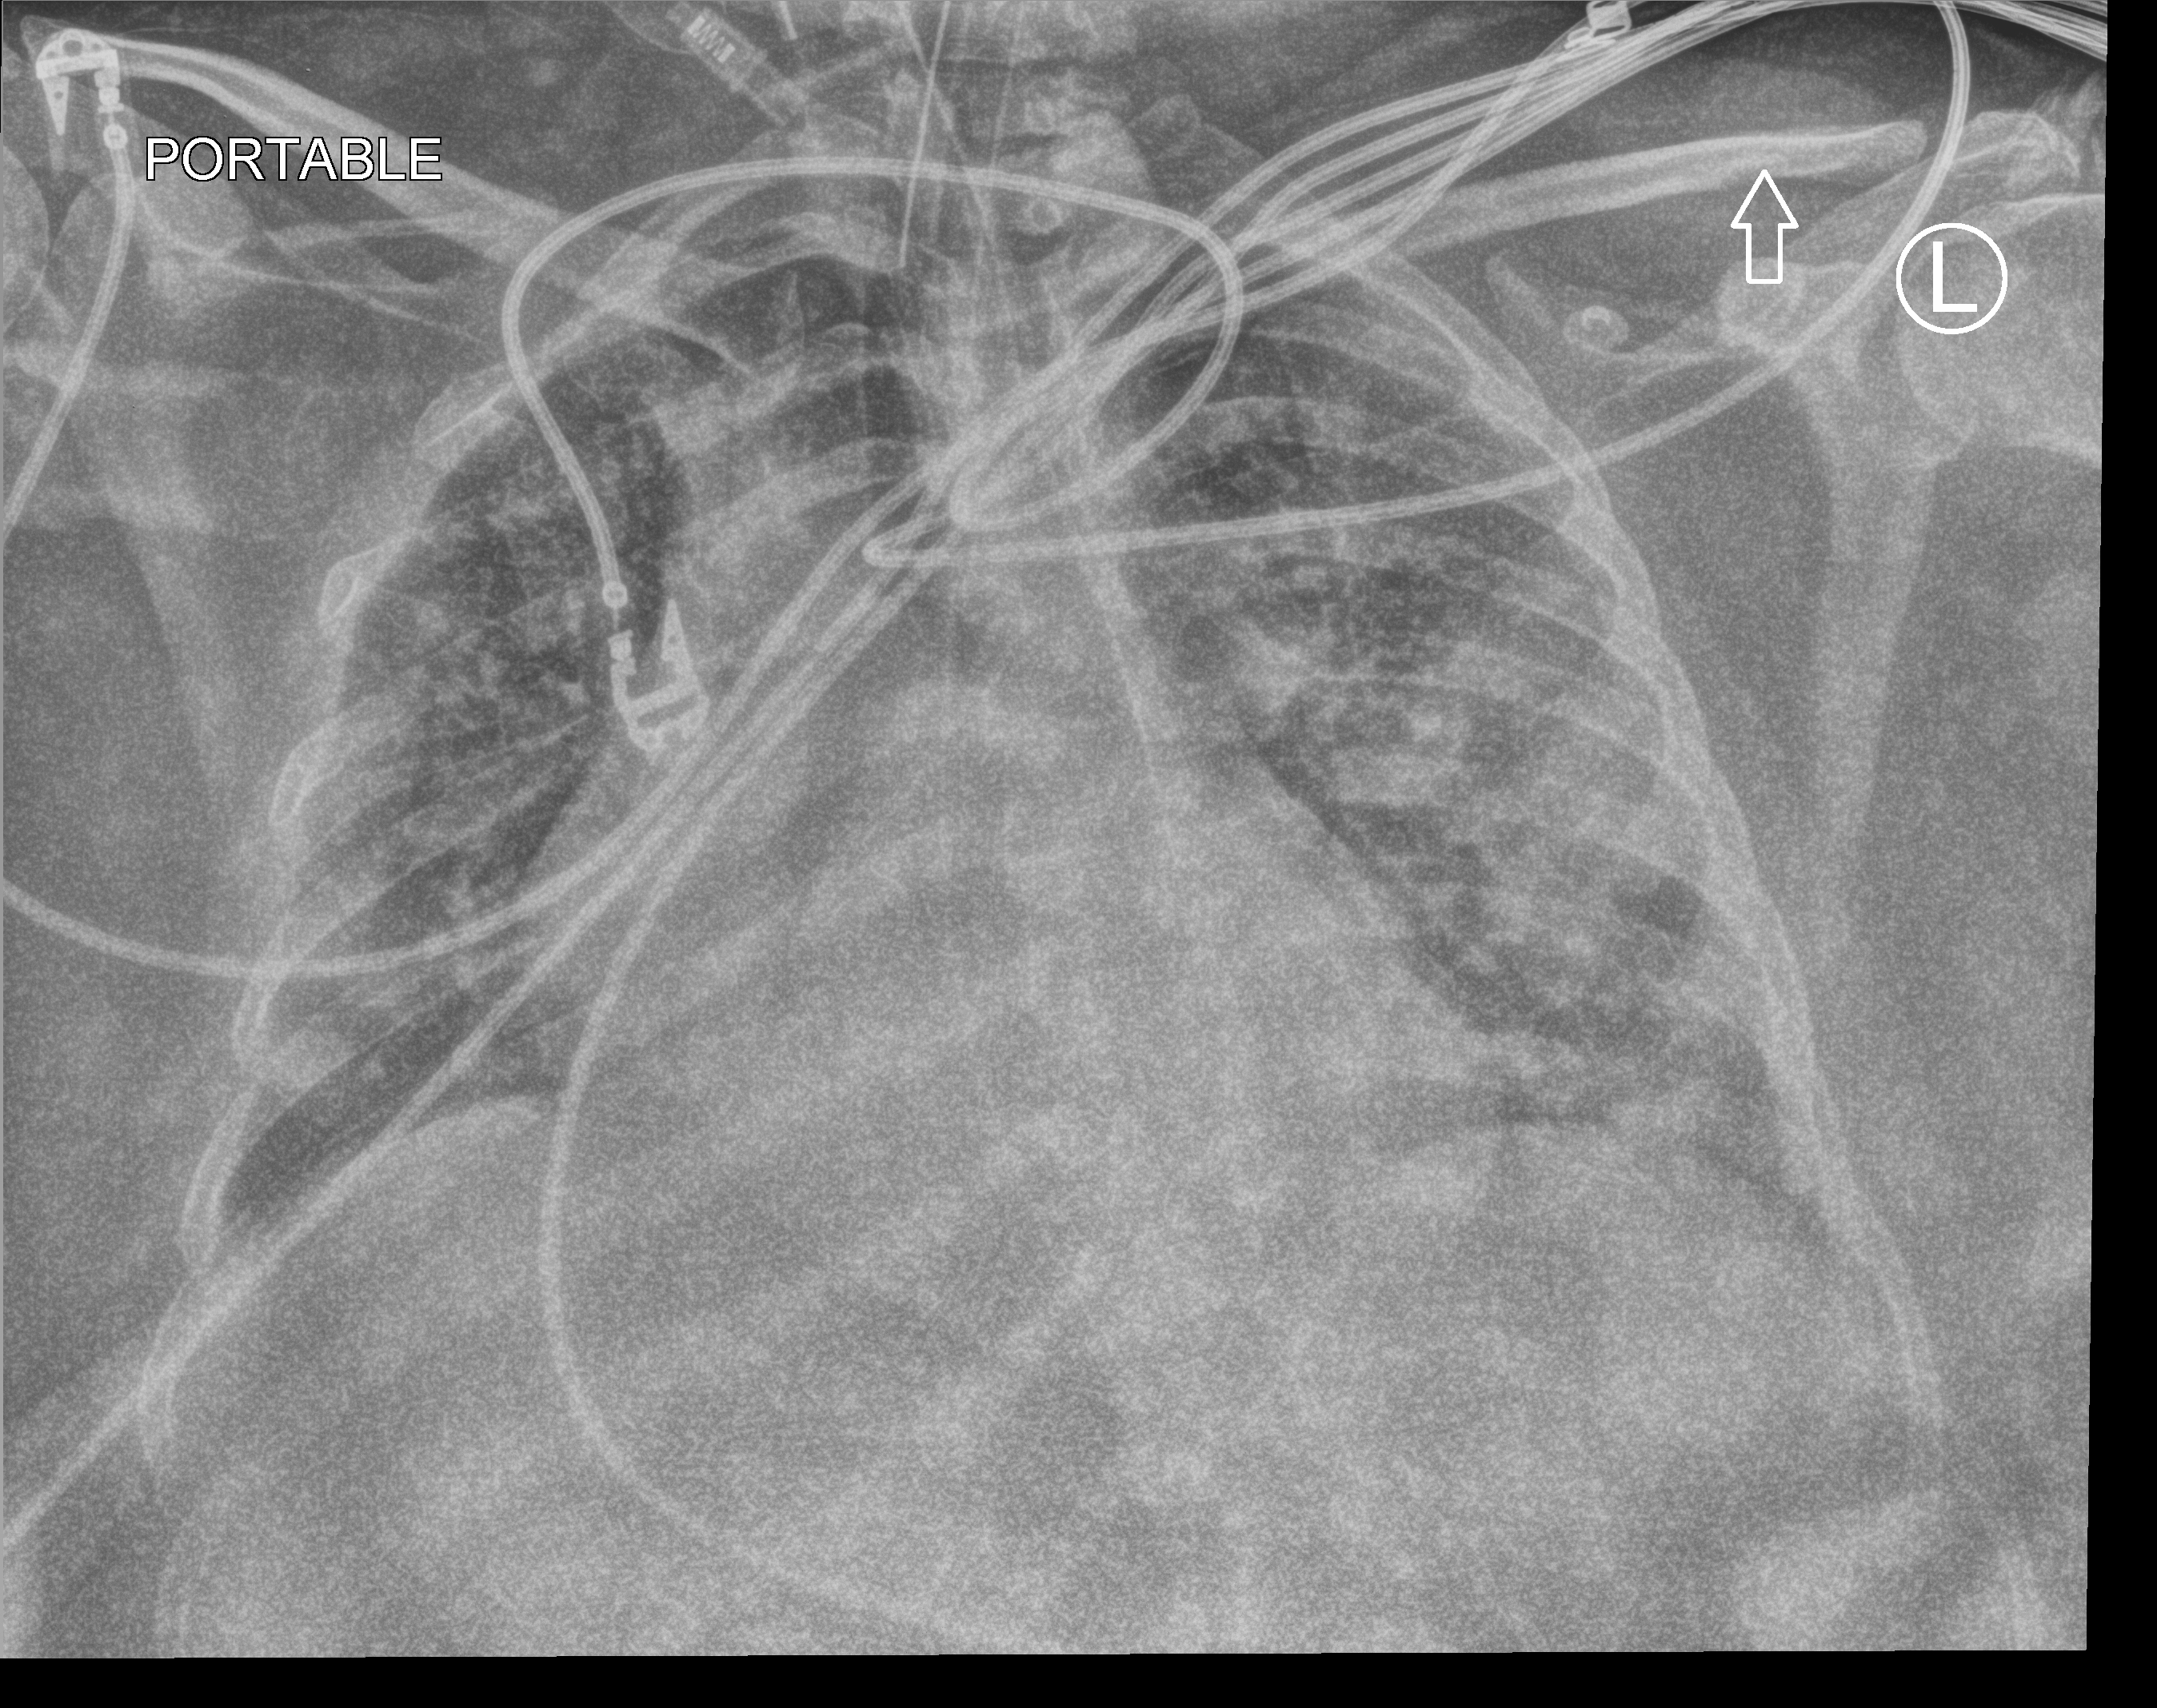
Chest X-ray (portable). Patient hospitalised with COVID-19; female, aged 18–59 years.
Admission-level facts for this patient (not findings on this image; timing relative to this image not recorded): length of hospital stay: 23 days; mechanically ventilated during this hospital stay: yes; admitted to intensive care during this hospital stay: yes.